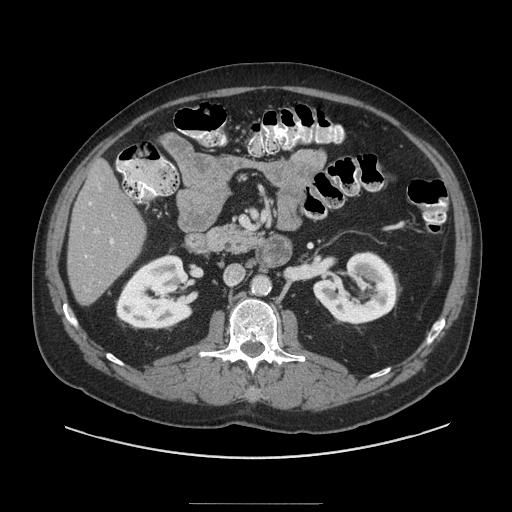
Contrast-enhanced abdominal CT (liver protocol), one axial slice; position 35 of 91 along the scan axis; 140 kVp; soft-tissue window (W 400 / L 40 HU); 512 × 512 image matrix, field of view 440 × 440 mm. From the clinical record (not read from this slice): diagnosis: hepatocellular carcinoma (patient treated with transarterial chemoembolisation; whether this scan precedes or follows treatment is not stated here); TNM stage (as recorded): Stage-I; Child-Pugh class: A; tumour differentiation: well differentiated; tumour nodularity: uninodular.
Structures marked on this image (semi-automatically segmented with operator editing):
- liver parenchyma outside the tumour (the mass and vessels are separate outlines, so this box may not span the whole liver): bounding box (x1, y1, x2, y2) in pixels: (68, 162, 146, 304)
- liver vessels: (89, 202, 114, 244)